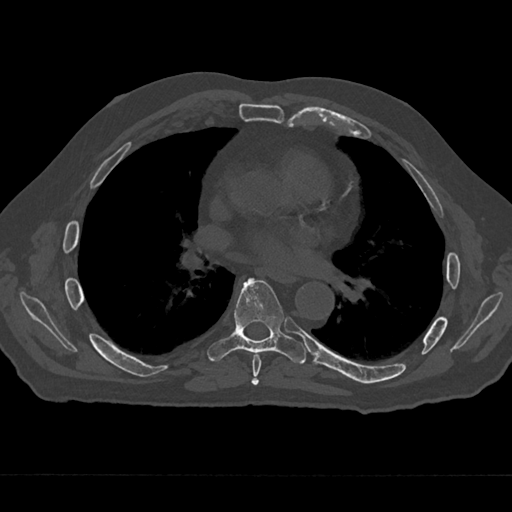
CT including the spine, one axial slice. Position 380 of 797 along the scan axis. Reconstruction kernel Br40s/3. Bone window (W 1800 / L 400 HU). 0.5 mm slice thickness. 512 × 512 image matrix, field of view 377 × 377 mm. Male patient, age 75 years. From the clinical record (not read from this slice): primary cancer: renal; vertebrae with lytic lesions (as recorded): T4.
Annotated regions visible in this slice (semi-automatically segmented with operator editing):
- T6 vertebra: bounding box [x1, y1, x2, y2] px = [252, 354, 262, 385]
- T7 vertebra: [207, 278, 307, 364]